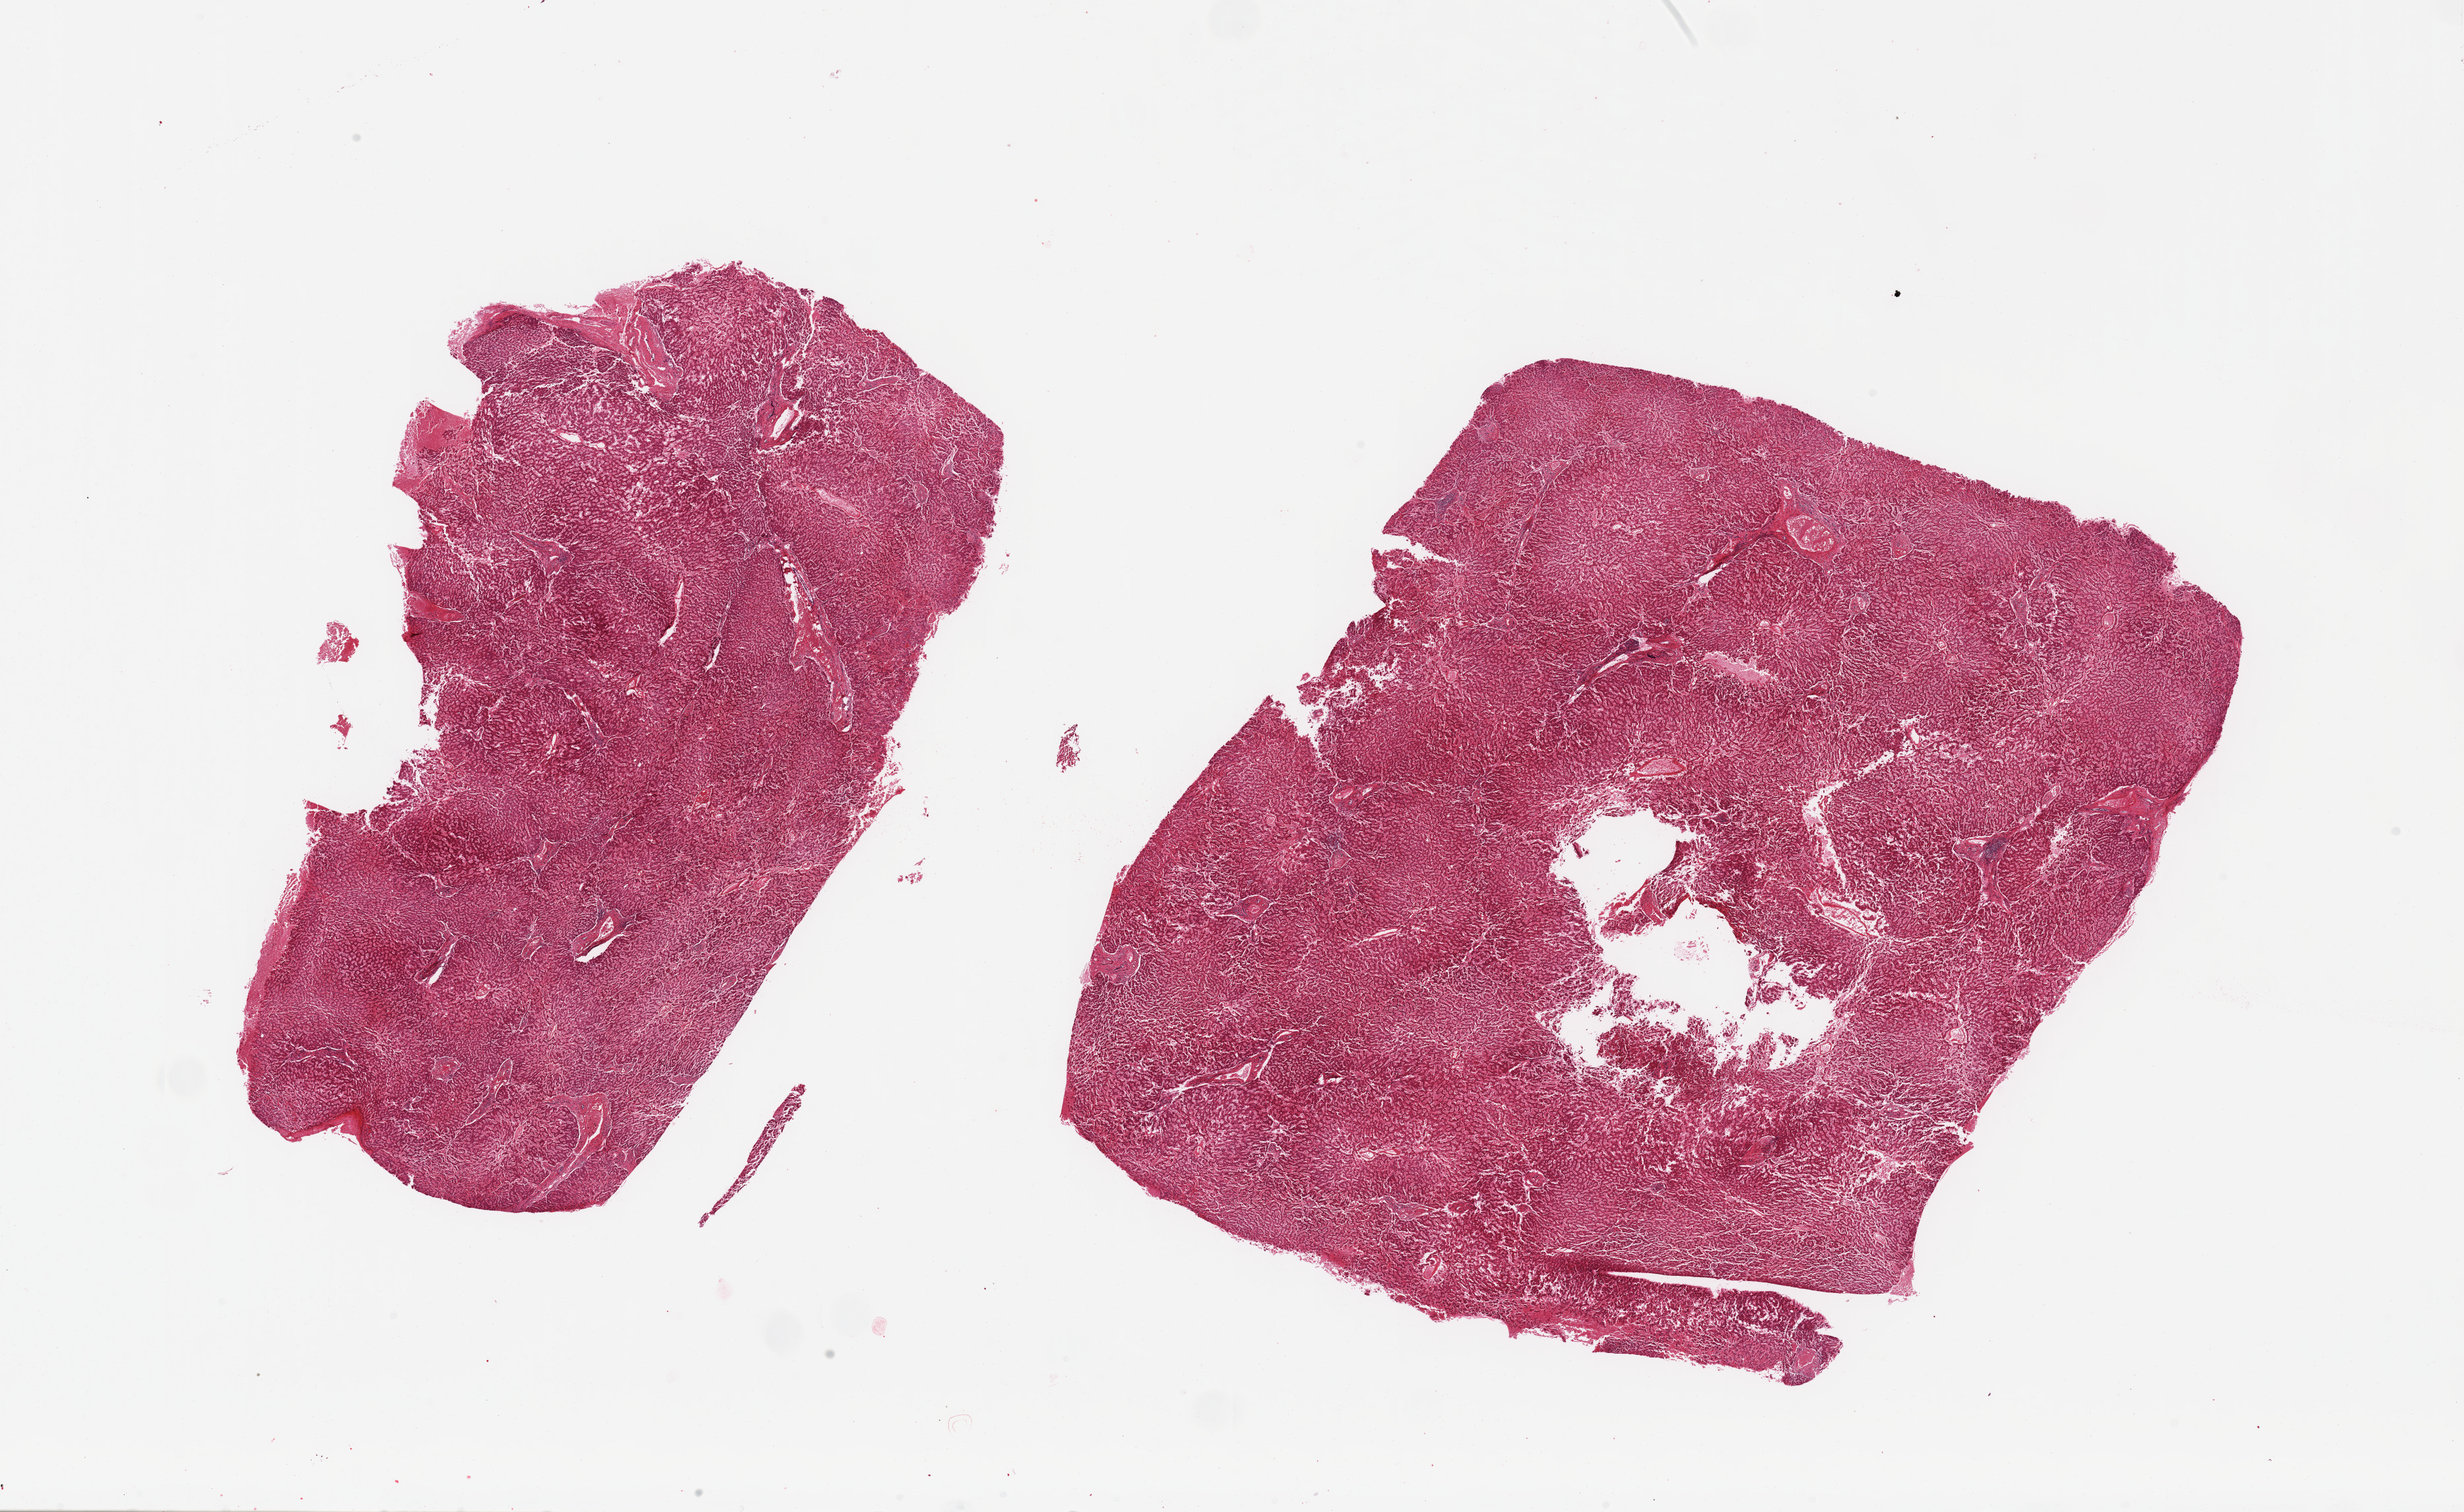
Haematoxylin and eosin whole-slide image, a low-resolution overview of the entire scanned area, about 29.5 x 18.1 mm; PAXgene-fixed paraffin-embedded (PFPE) section; sampled site (target tissue): liver; tissue donor sample. Male donor.
- review note (as recorded): 2 pieces; occasional portal lymphoid collections; no cirrhosis; poorly preserved and fragmented parenchyma